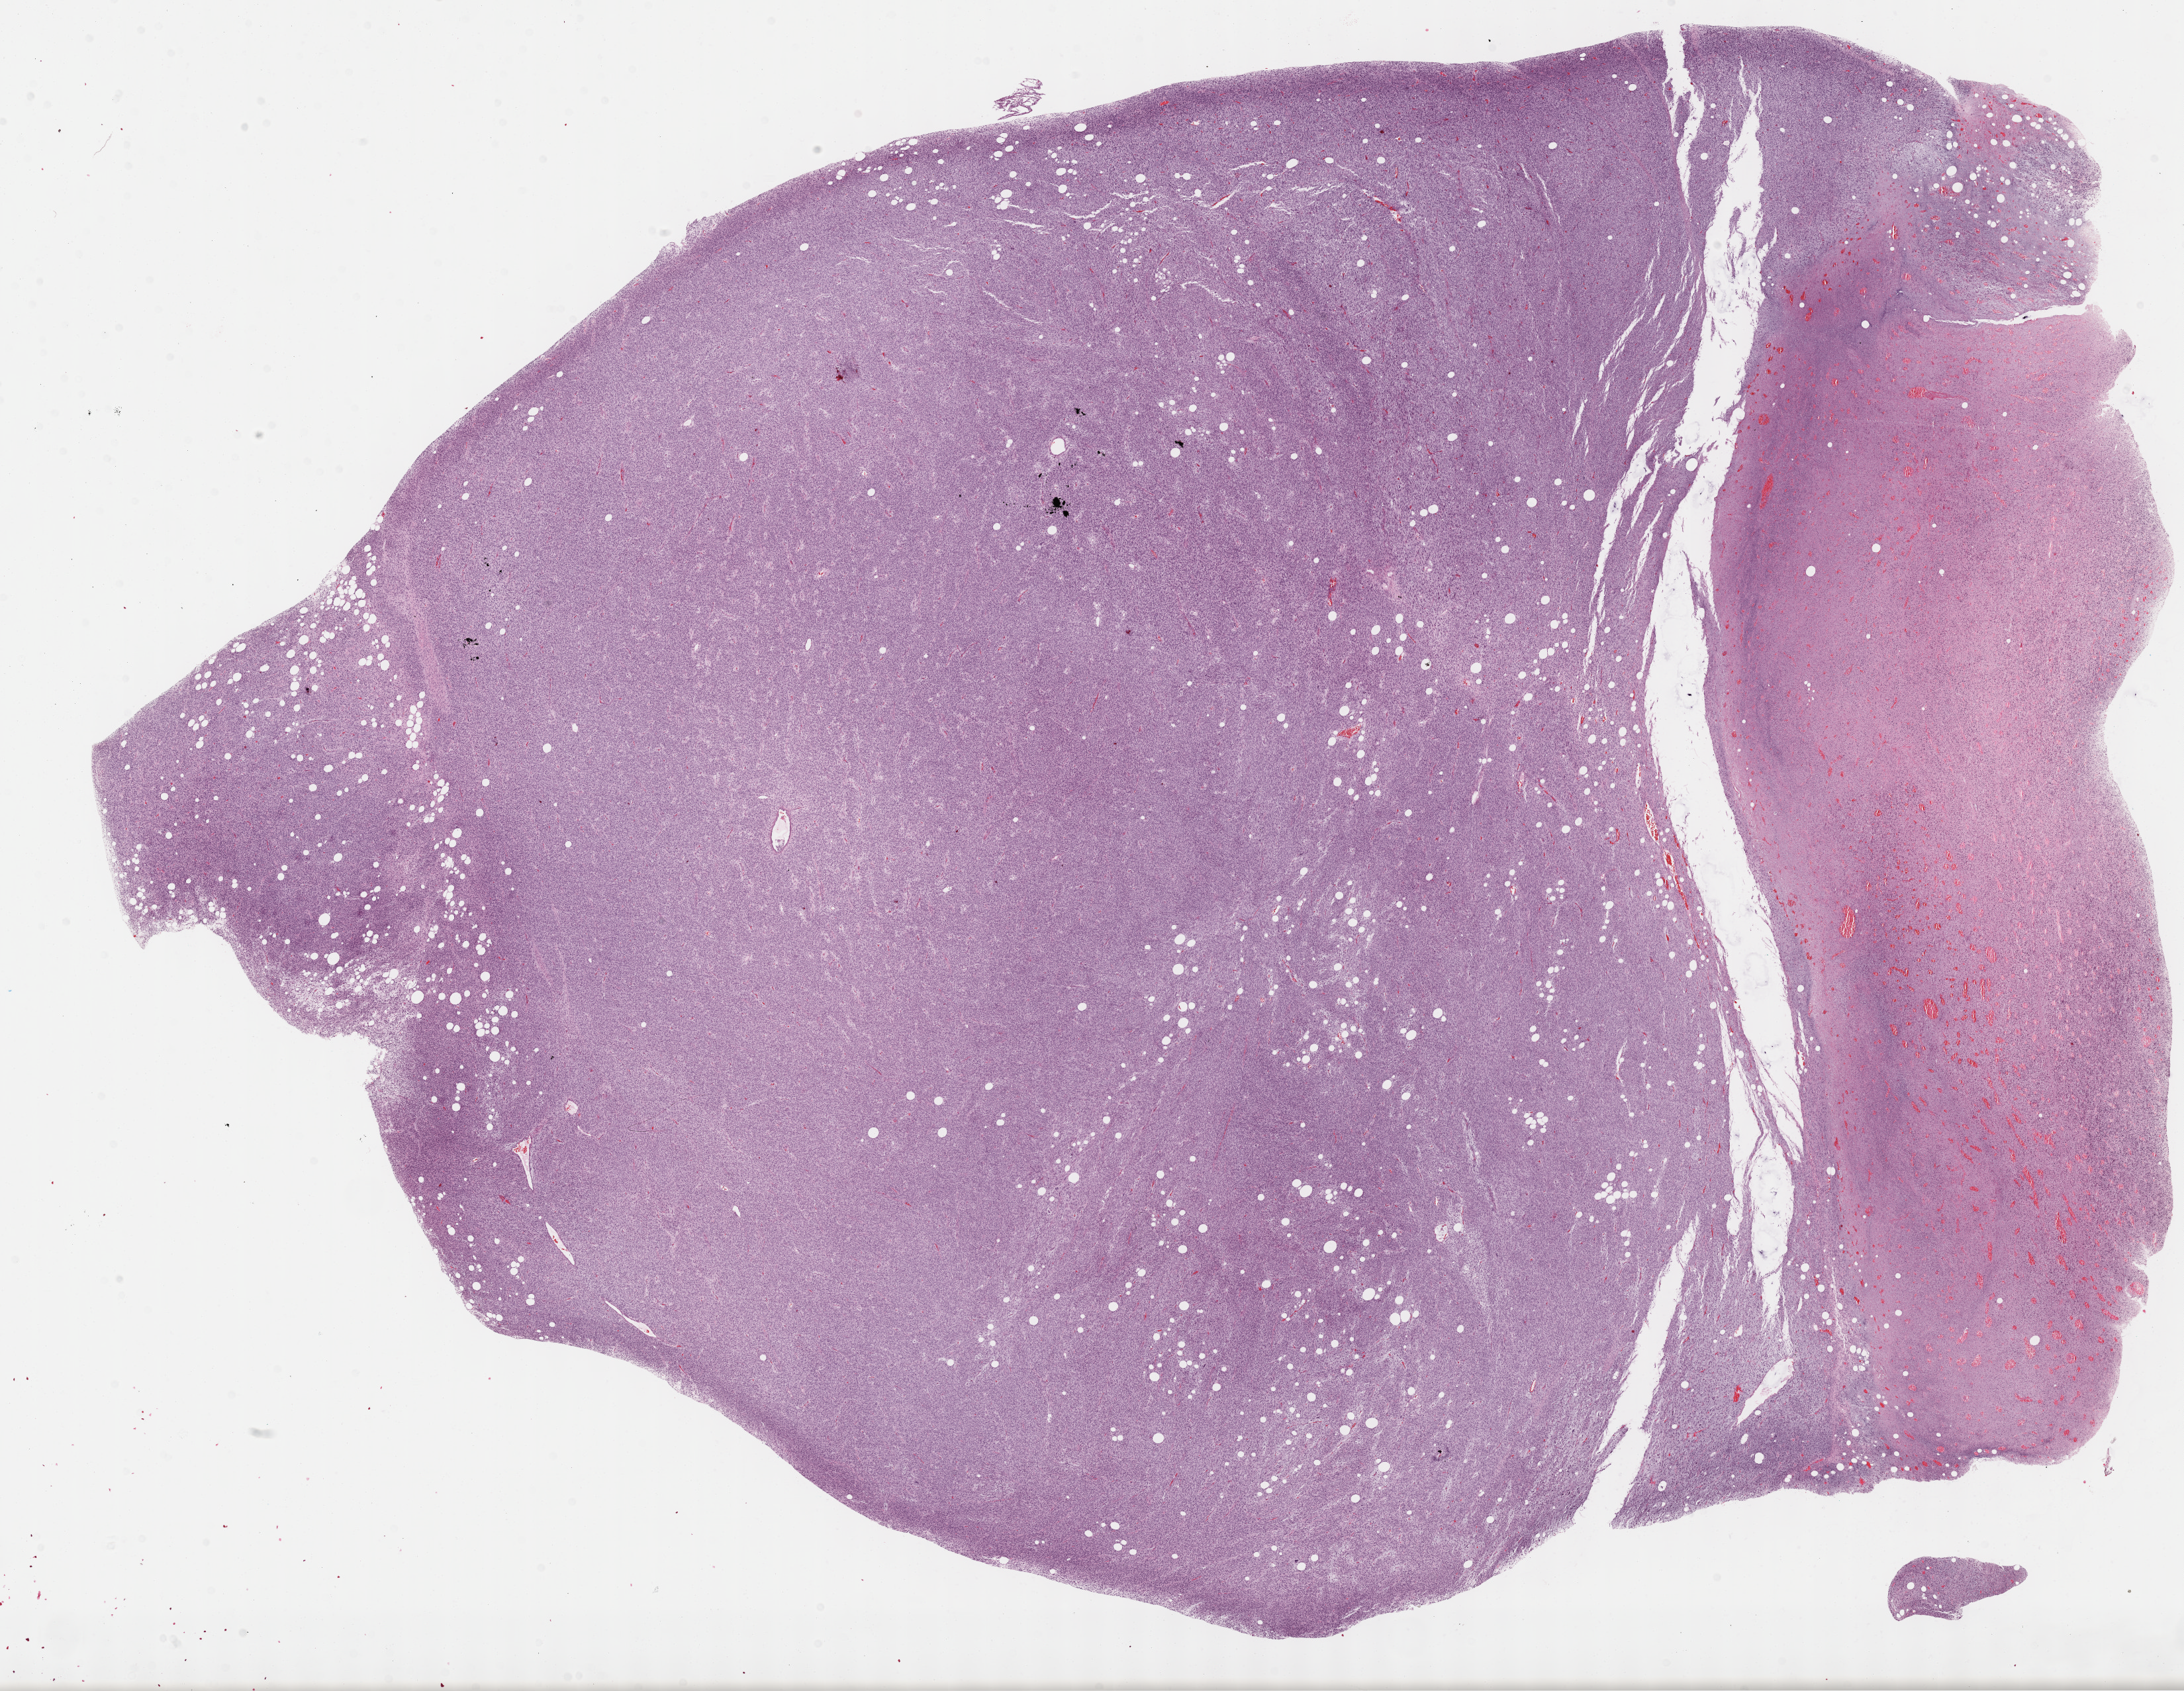
Digitized Hematoxylin and eosin (H&E) stained tissue section (whole slide) — a low-resolution overview of the entire scanned area, about 26.7 x 20.7 mm. Formalin-fixed paraffin-embedded (FFPE) diagnostic section. Retroperitoneum and peritoneum, primary tumour sample. Patient: male, age at initial diagnosis 80 years.
Pathologic diagnosis: Dedifferentiated liposarcoma (retroperitoneum).